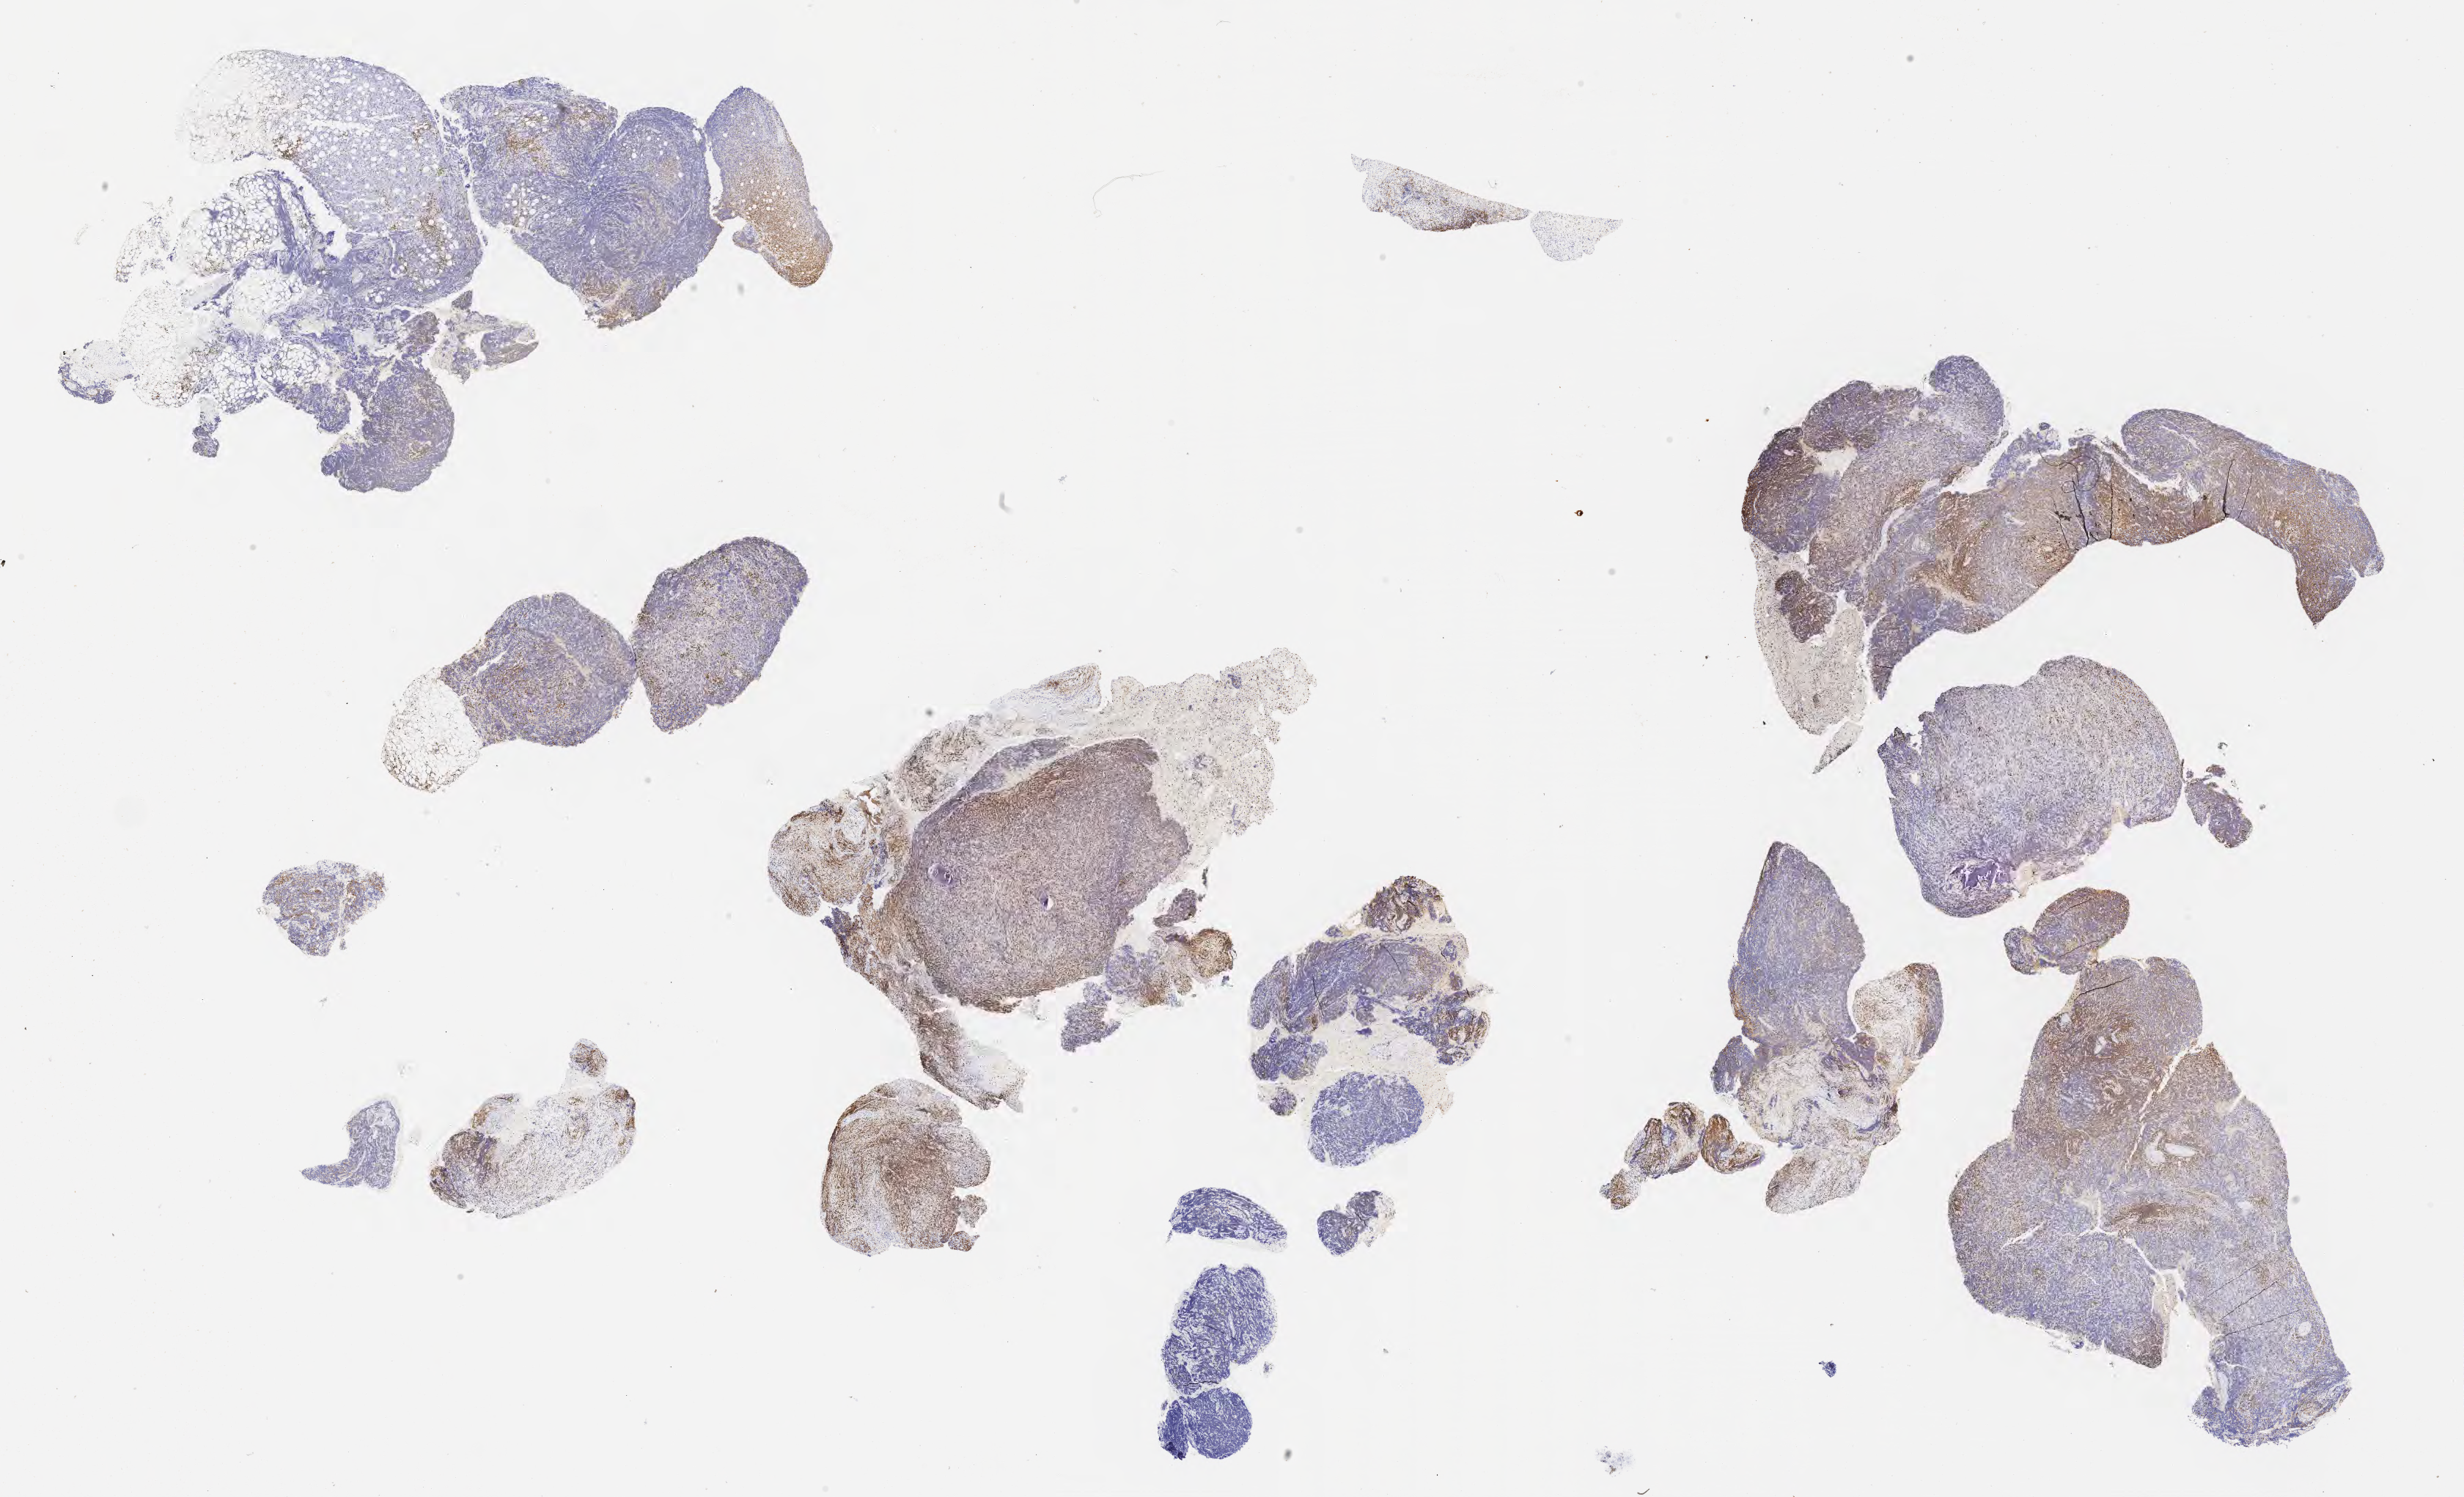
Immunohistochemistry (IHC) whole-slide image stained for CD3, a low-resolution overview of the entire scanned area, about 27.2 x 16.5 mm; specimen: tumor tissue. Patient: male, 45 years old.
- diagnosis: Diffuse large B-cell lymphoma, NOS